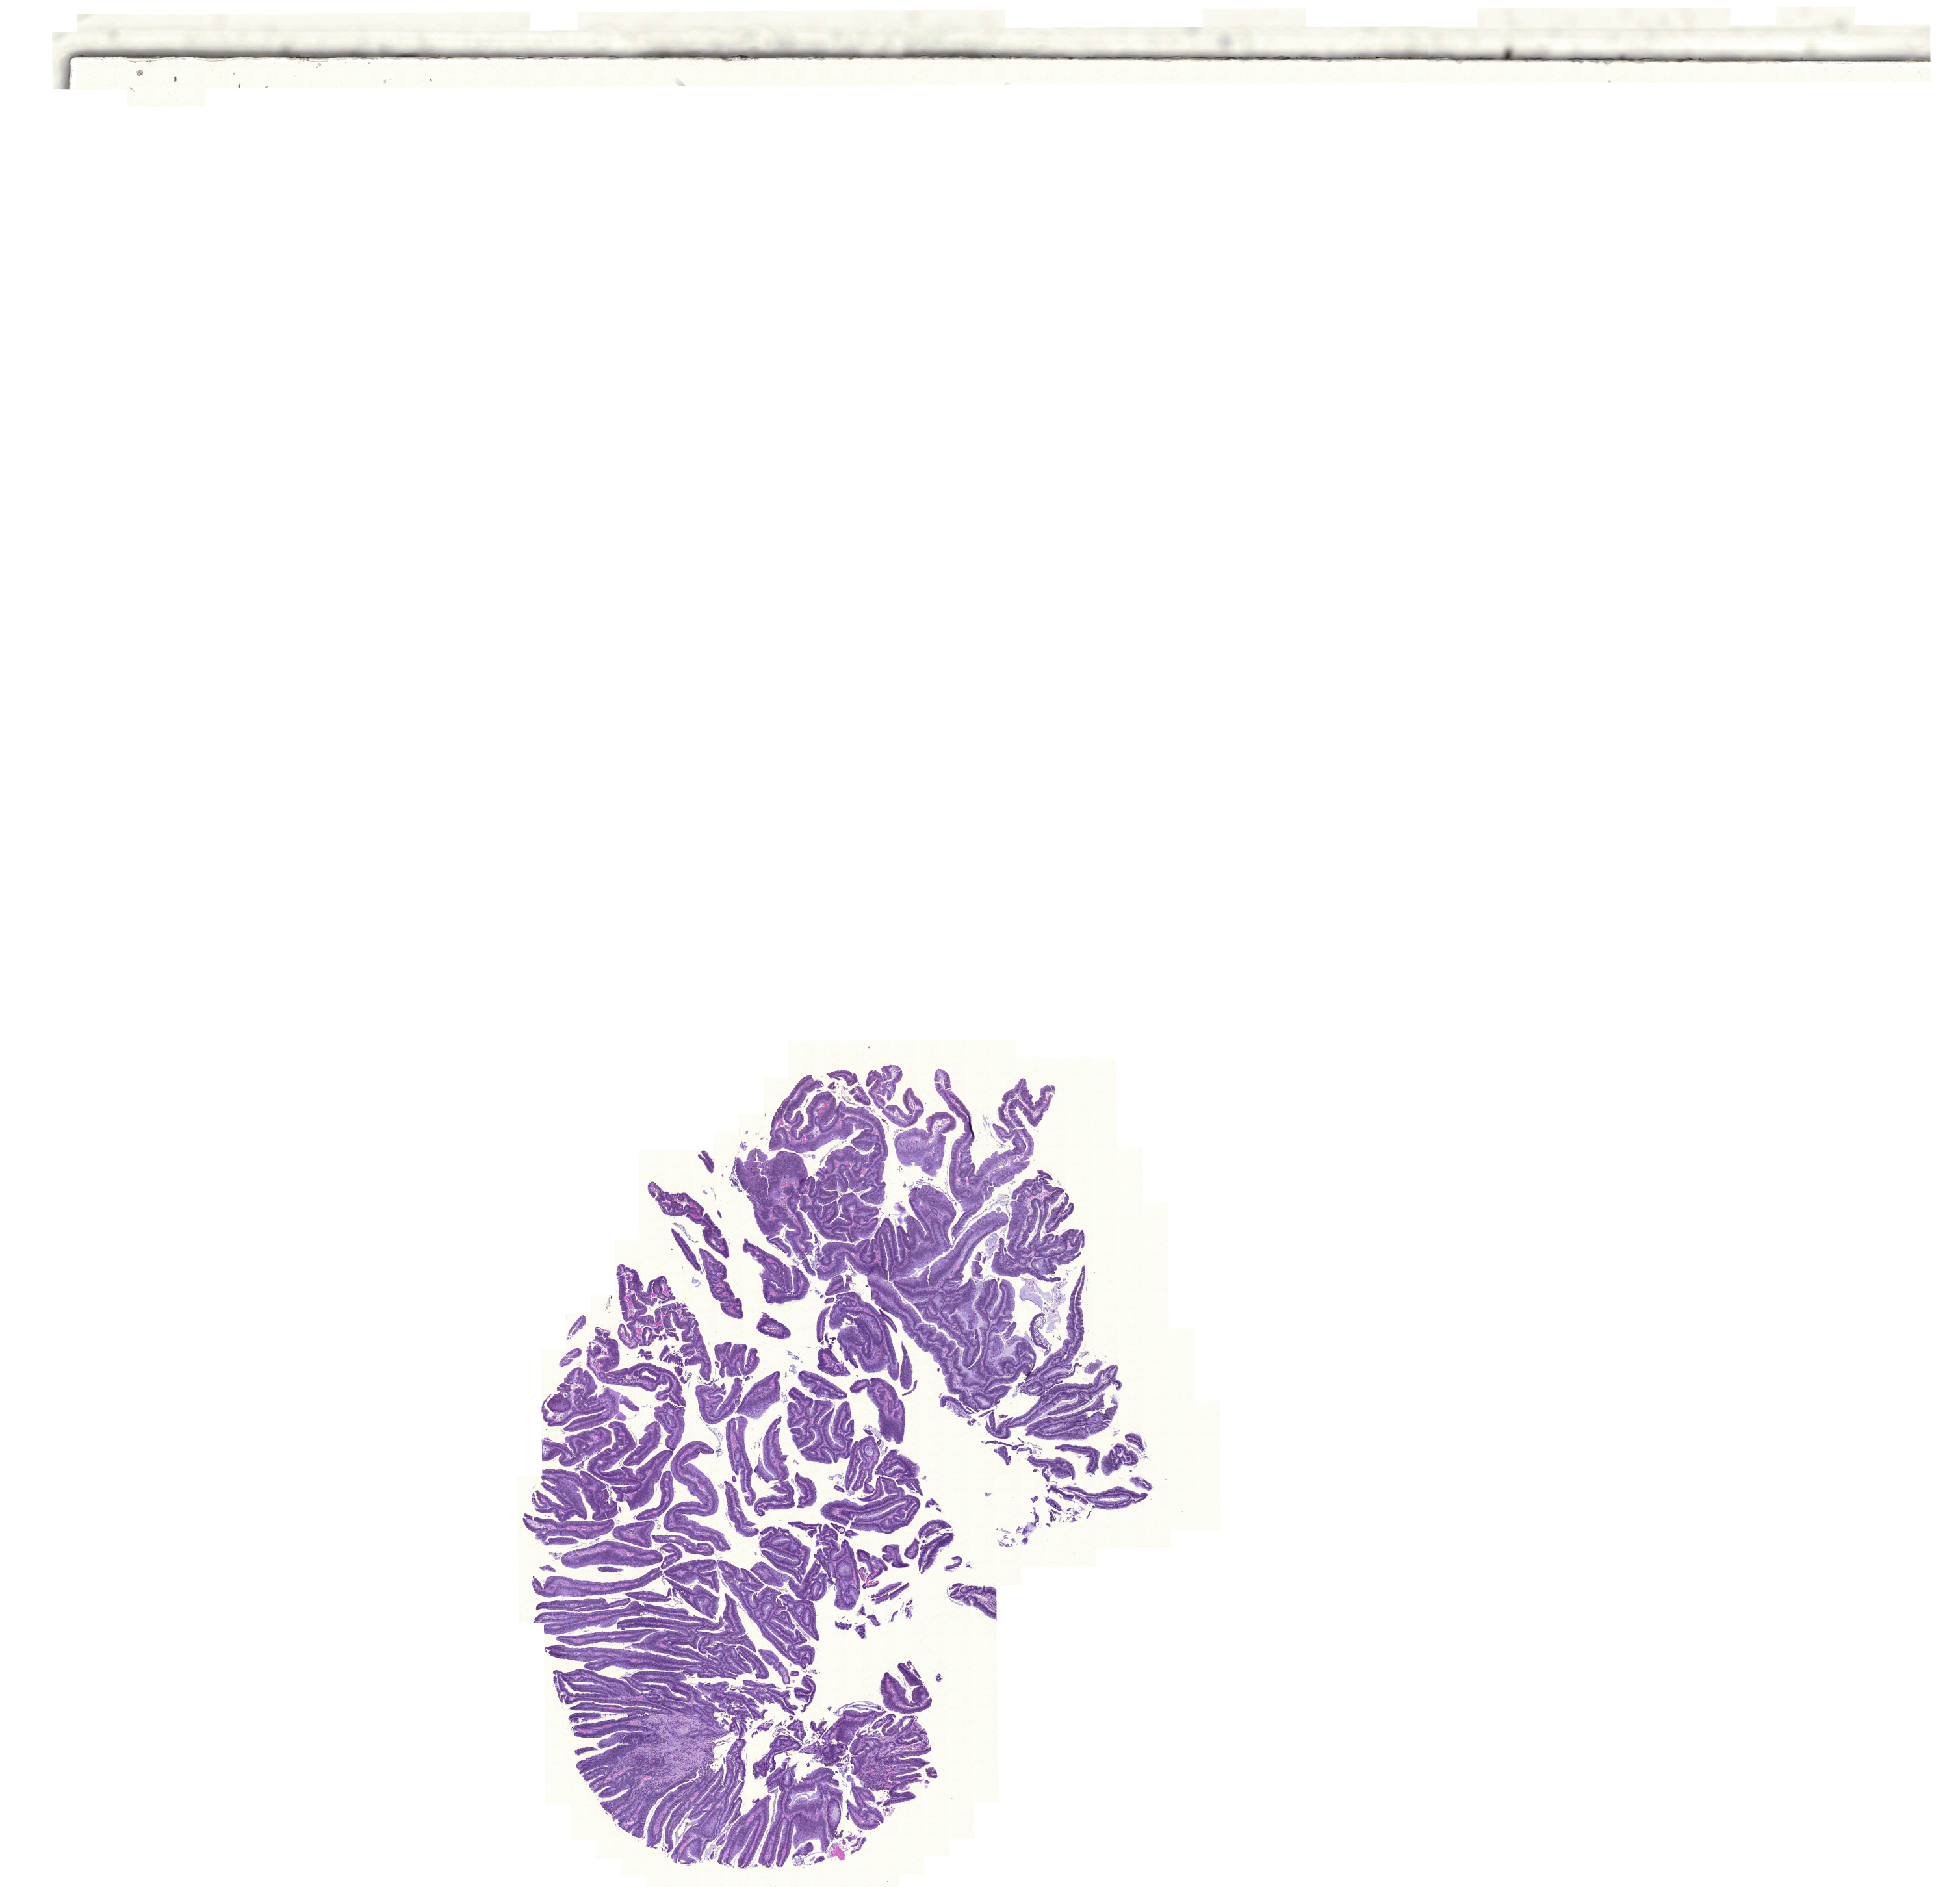
Digitized H&E tissue section (whole slide) — low-resolution overview of the scanned area, about 22.4 x 21.6 mm (slide scanned at 20x), formalin-fixed paraffin-embedded (FFPE) diagnostic section, sample: primary tumour, colon. Patient: male, age at initial diagnosis 73 years.
Pathologic diagnosis: Adenocarcinoma, NOS (cecum). AJCC pathologic stage: I (6th edition). Lymph nodes positive (case pathology): 0 of 18 examined.